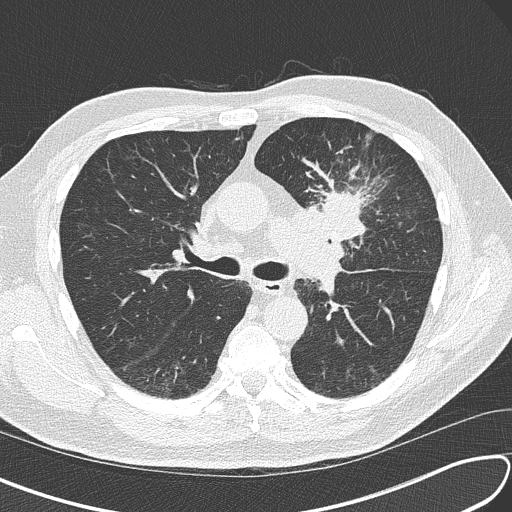
Chest CT (low-dose screening protocol), one axial image, third screening round (two years after baseline), lung window (W 1500 / L -600 HU), lung (sharp) reconstruction kernel (B50f), 120 kVp, slice 60 of 156 in the series. Male participant, aged 67 years at enrolment.
Expert-annotated lung lesion, box from (x=296, y=167) to (x=397, y=259) px. Screening reader's record for this exam (one nodule recorded; not confirmed to be the boxed lesion): non-calcified nodule or mass ≥4 mm, left upper lobe, 30 × 23 mm, soft tissue attenuation, pre-existing on the prior screen: no. Official screen result: positive, other. Later outcome: lung cancer diagnosed 41 days after this screen — small cell carcinoma, NOS, left upper lobe, stage IV (AJCC 6th edition), 30 mm at pathology.